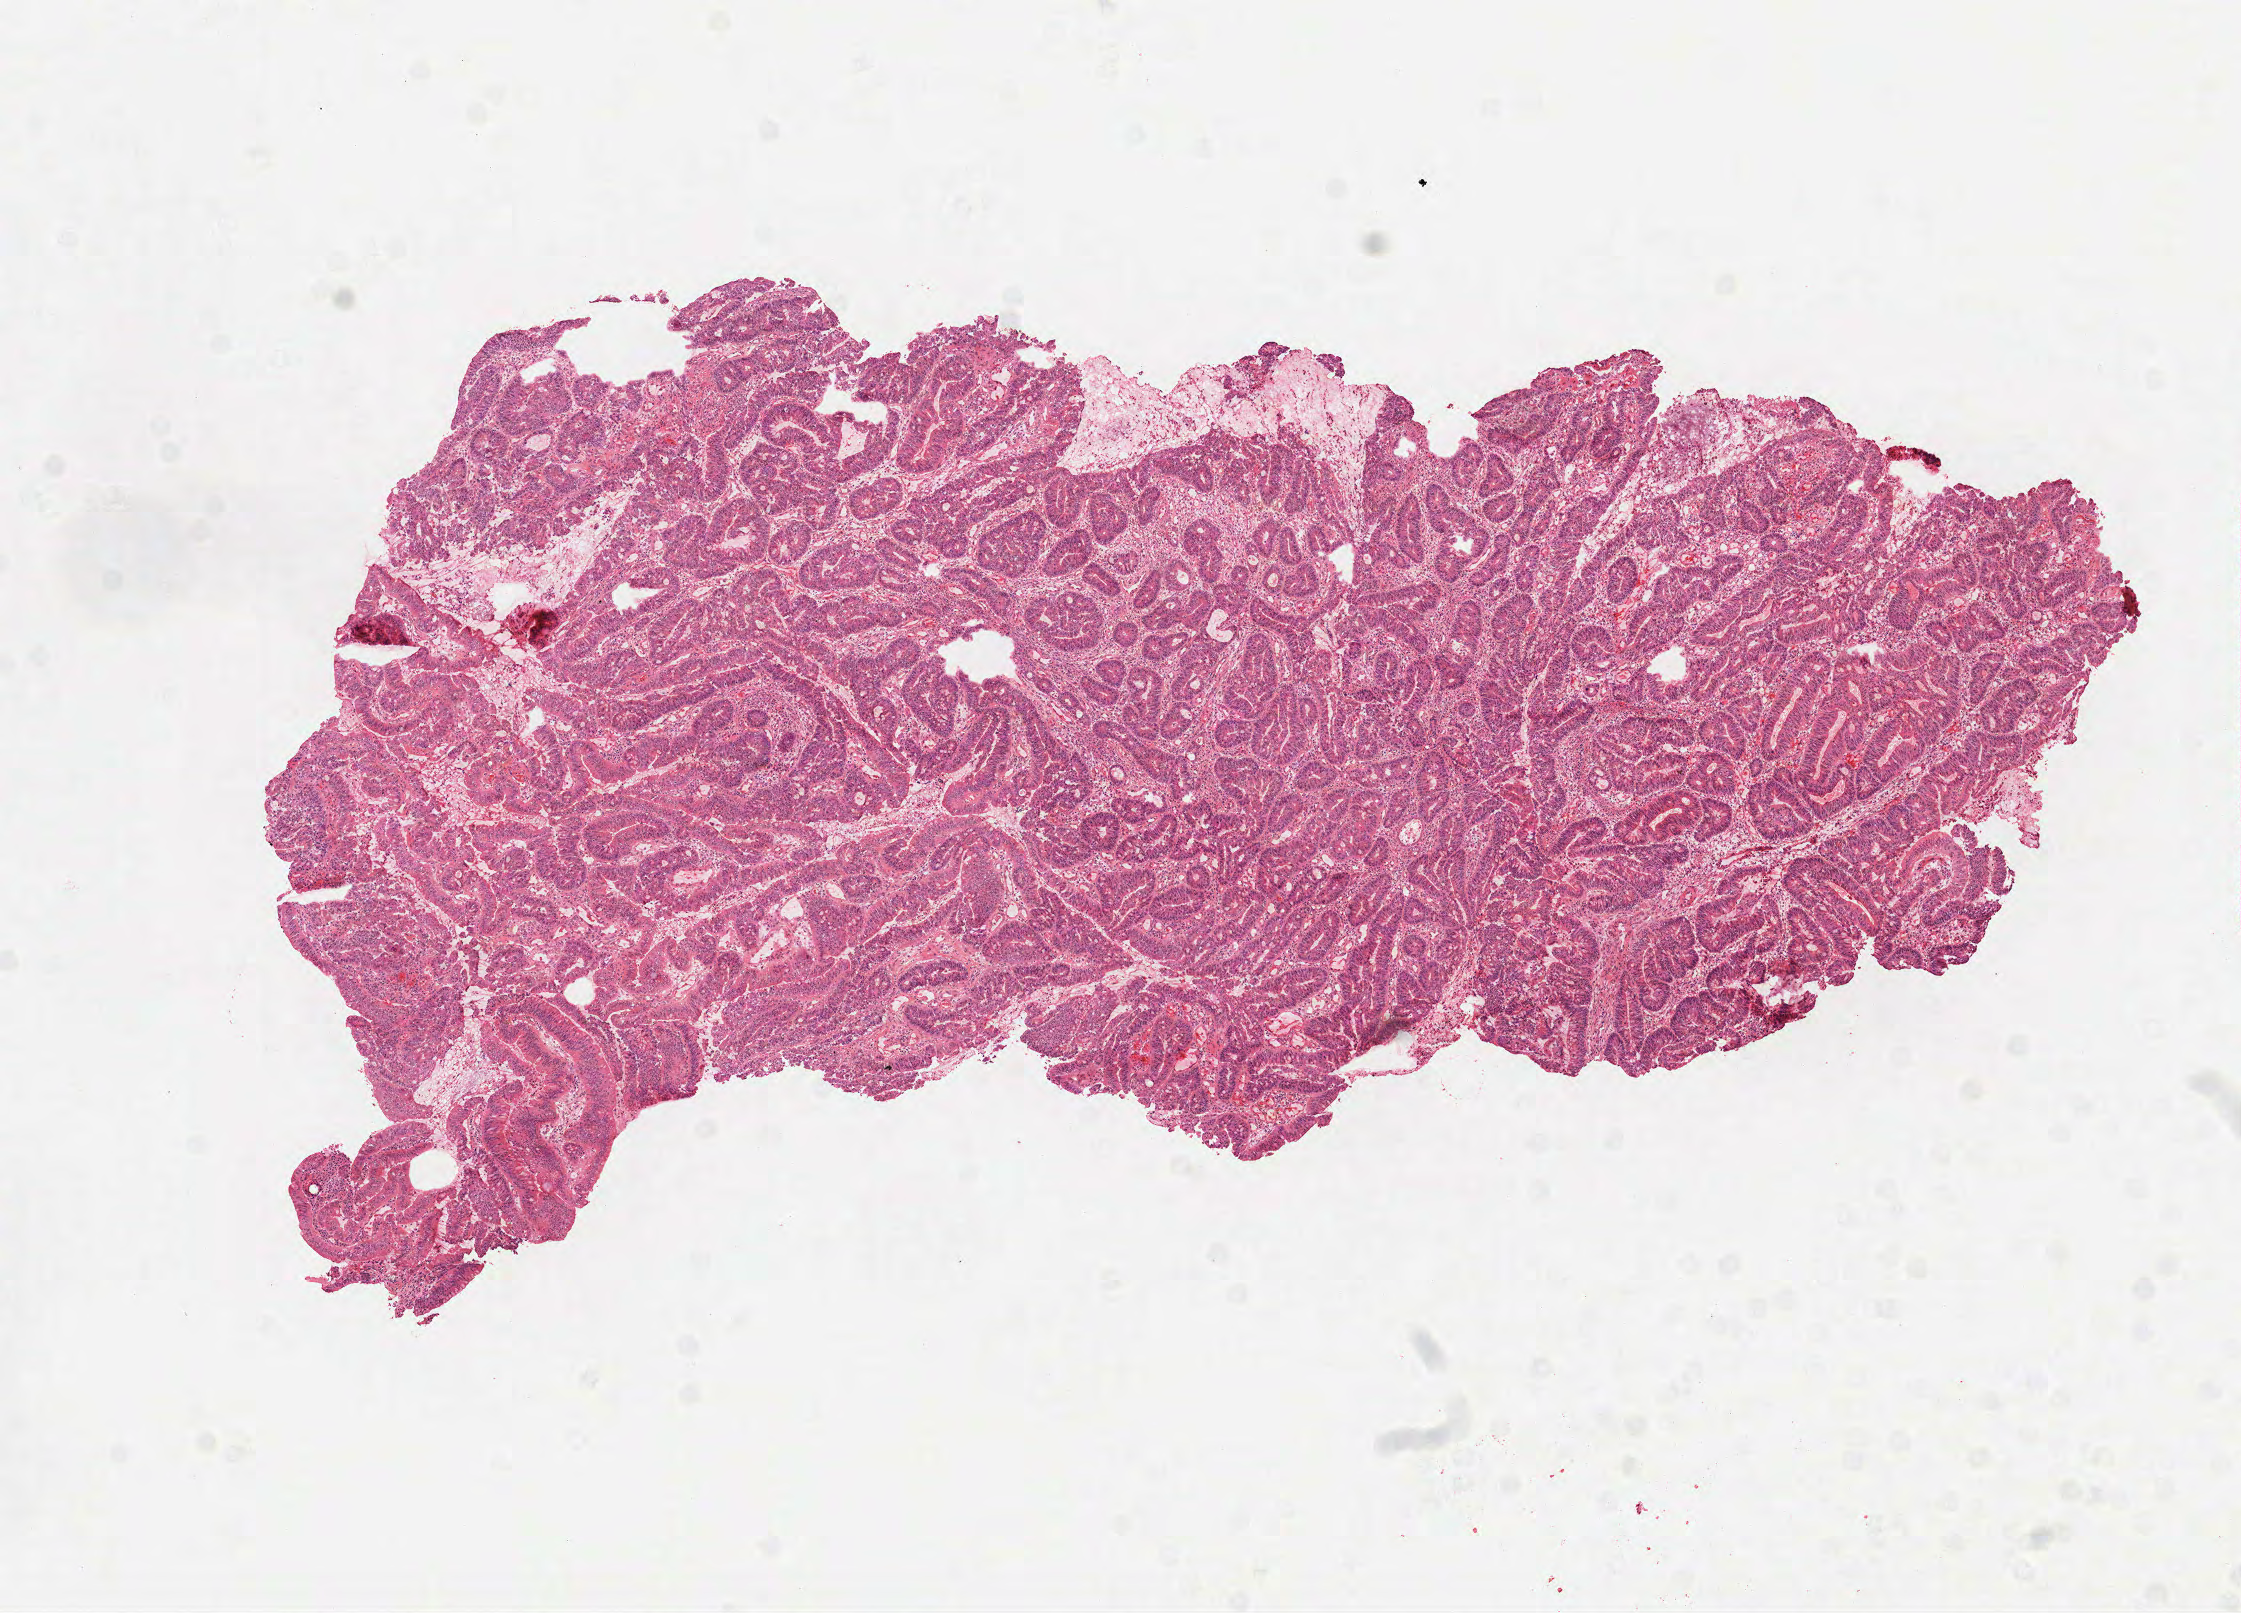
Digitized H&E tissue section (whole slide), shown as a low-resolution overview of the whole scanned area (about 9.0 x 6.5 mm); frozen section from the top of the tissue portion; sample: primary tumour, colon. Female patient. Slide review estimates, as recorded: tumour cells 85%, tumour nuclei 75%, normal cells 0%, stromal cells 15%, necrosis 0%.
AJCC pathologic stage: IIA (6th edition). Pathologic diagnosis: Adenocarcinoma, NOS (cecum).